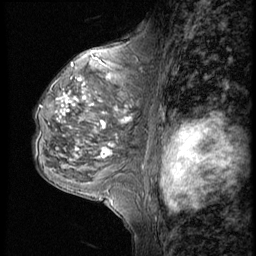
Breast MRI (dynamic contrast-enhanced), one sagittal slice. Slice 32 of 56 in the series (ordered by position). 4 images stored at this slice position (order not interpretable as contrast timing). 1.5 T. TE 4.2 ms, TR 9 ms. 256 × 256 image matrix, field of view 180 × 180 mm. Female patient, age 50 years. Case-level facts recorded for this patient, not image findings: setting: breast cancer imaged before/during neoadjuvant chemotherapy; receptor status: triple-negative.
Annotated regions visible in this slice (semi-automatic segmentation, software-assisted and operator-edited):
- analysis volume of interest (the breast-tissue region the enhancement analysis was run in; not a lesion): bounding box (x1, y1, x2, y2) in pixels: (32, 46, 148, 188)
- tumour enhancement mask (voxels above the 140 % enhancement threshold inside the analysis volume of interest): (63, 77, 132, 157)